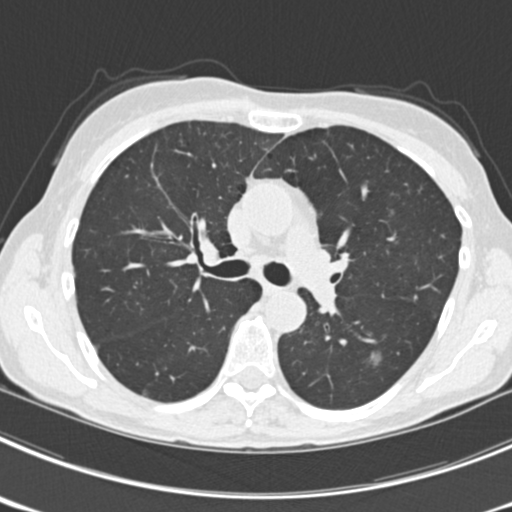
Axial slice from a low-dose chest CT screening exam. Third screening round (two years after baseline). Lung window (W 1500 / L -600 HU). Standard (soft-tissue) reconstruction kernel (B30f). 120 kVp. Slice 78 of 225 in the series. 512 × 512 image matrix, field of view 302 × 302 mm. Female participant, aged 63 years at enrolment.
Expert reader's lesion annotation, box from (x=357, y=341) to (x=396, y=381) px. The screening reader recorded 9 non-calcified nodules or masses ≥4 mm on this exam (left upper lobe, right upper lobe, left upper lobe, left lower lobe, right middle lobe, left lower lobe, left lower lobe, right lower lobe, right lower lobe); which of them this box marks is not recorded. Participant outcome: lung cancer diagnosed 15 days after this screen — bronchiolo-alveolar adenocarcinoma, NOS, right upper lobe, right middle lobe, right lower lobe, left upper lobe, left lower lobe, moderately differentiated (G2), stage IV (AJCC 6th edition).